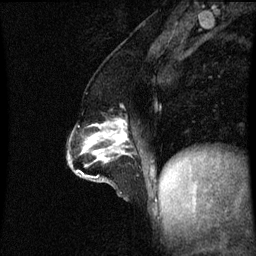
Breast MRI (dynamic contrast-enhanced), one sagittal slice. Position 27 of 60 along the scan axis. Dynamic contrast-enhanced series, image 2 of 3 at this slice position (ordered by acquisition). 1.5 T. TE 4.2 ms, TR 8.9 ms. 256 × 256 image matrix, field of view 200 × 200 mm. Patient: female, 47 years. Case-level facts recorded for this patient, not image findings: setting: breast cancer imaged before/during neoadjuvant chemotherapy; receptor status: HR-positive, HER2-negative.
Structures marked on this image (semi-automatic segmentation, software-assisted and operator-edited):
- analysis volume of interest (the breast-tissue region the enhancement analysis was run in; not a lesion): bounding box <71,120,130,163> (left, top, right, bottom; pixels)
- tumour enhancement mask (voxels above the 70 % enhancement threshold inside the analysis volume of interest): <96,122,128,143>